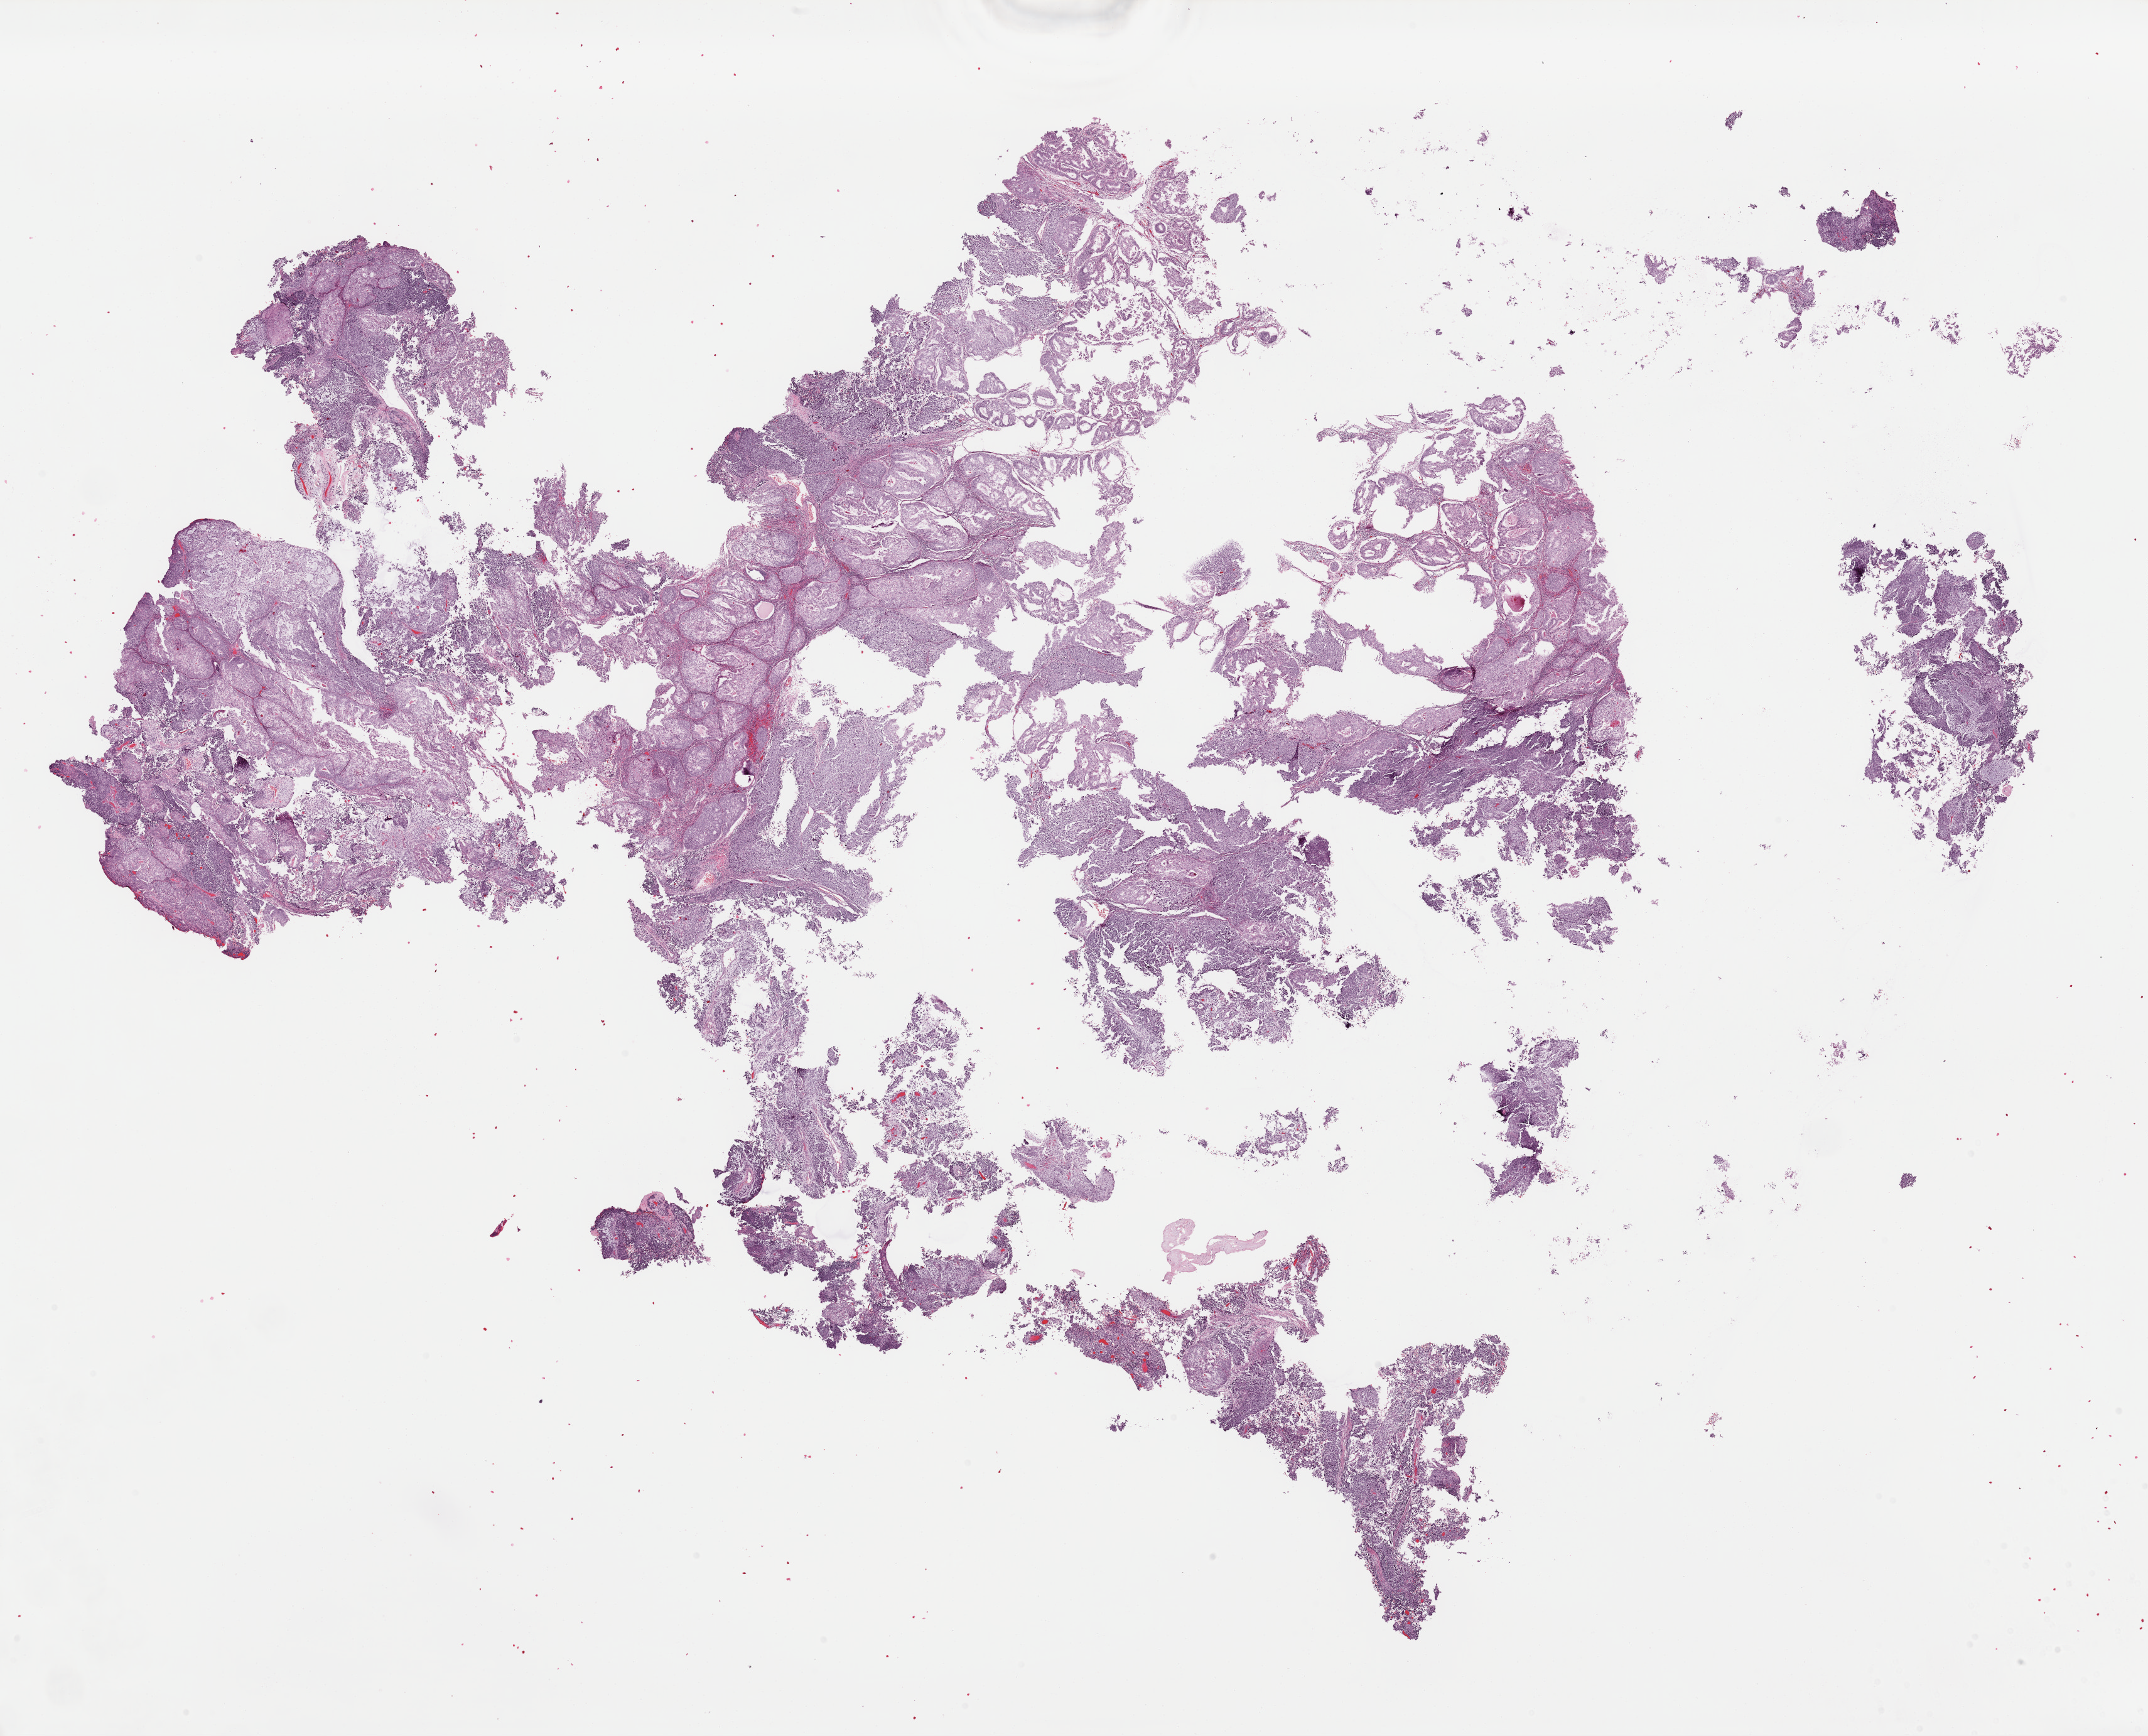
H&E-stained whole-slide image — a low-resolution overview of the entire scanned area, about 27.0 x 21.8 mm (slide scanned at 40x); formalin-fixed paraffin-embedded (FFPE) diagnostic section; uterus, primary tumour sample. Patient: female, age at initial diagnosis 67 years.
Diagnosis: Mullerian mixed tumor (endometrium). FIGO stage: IA.